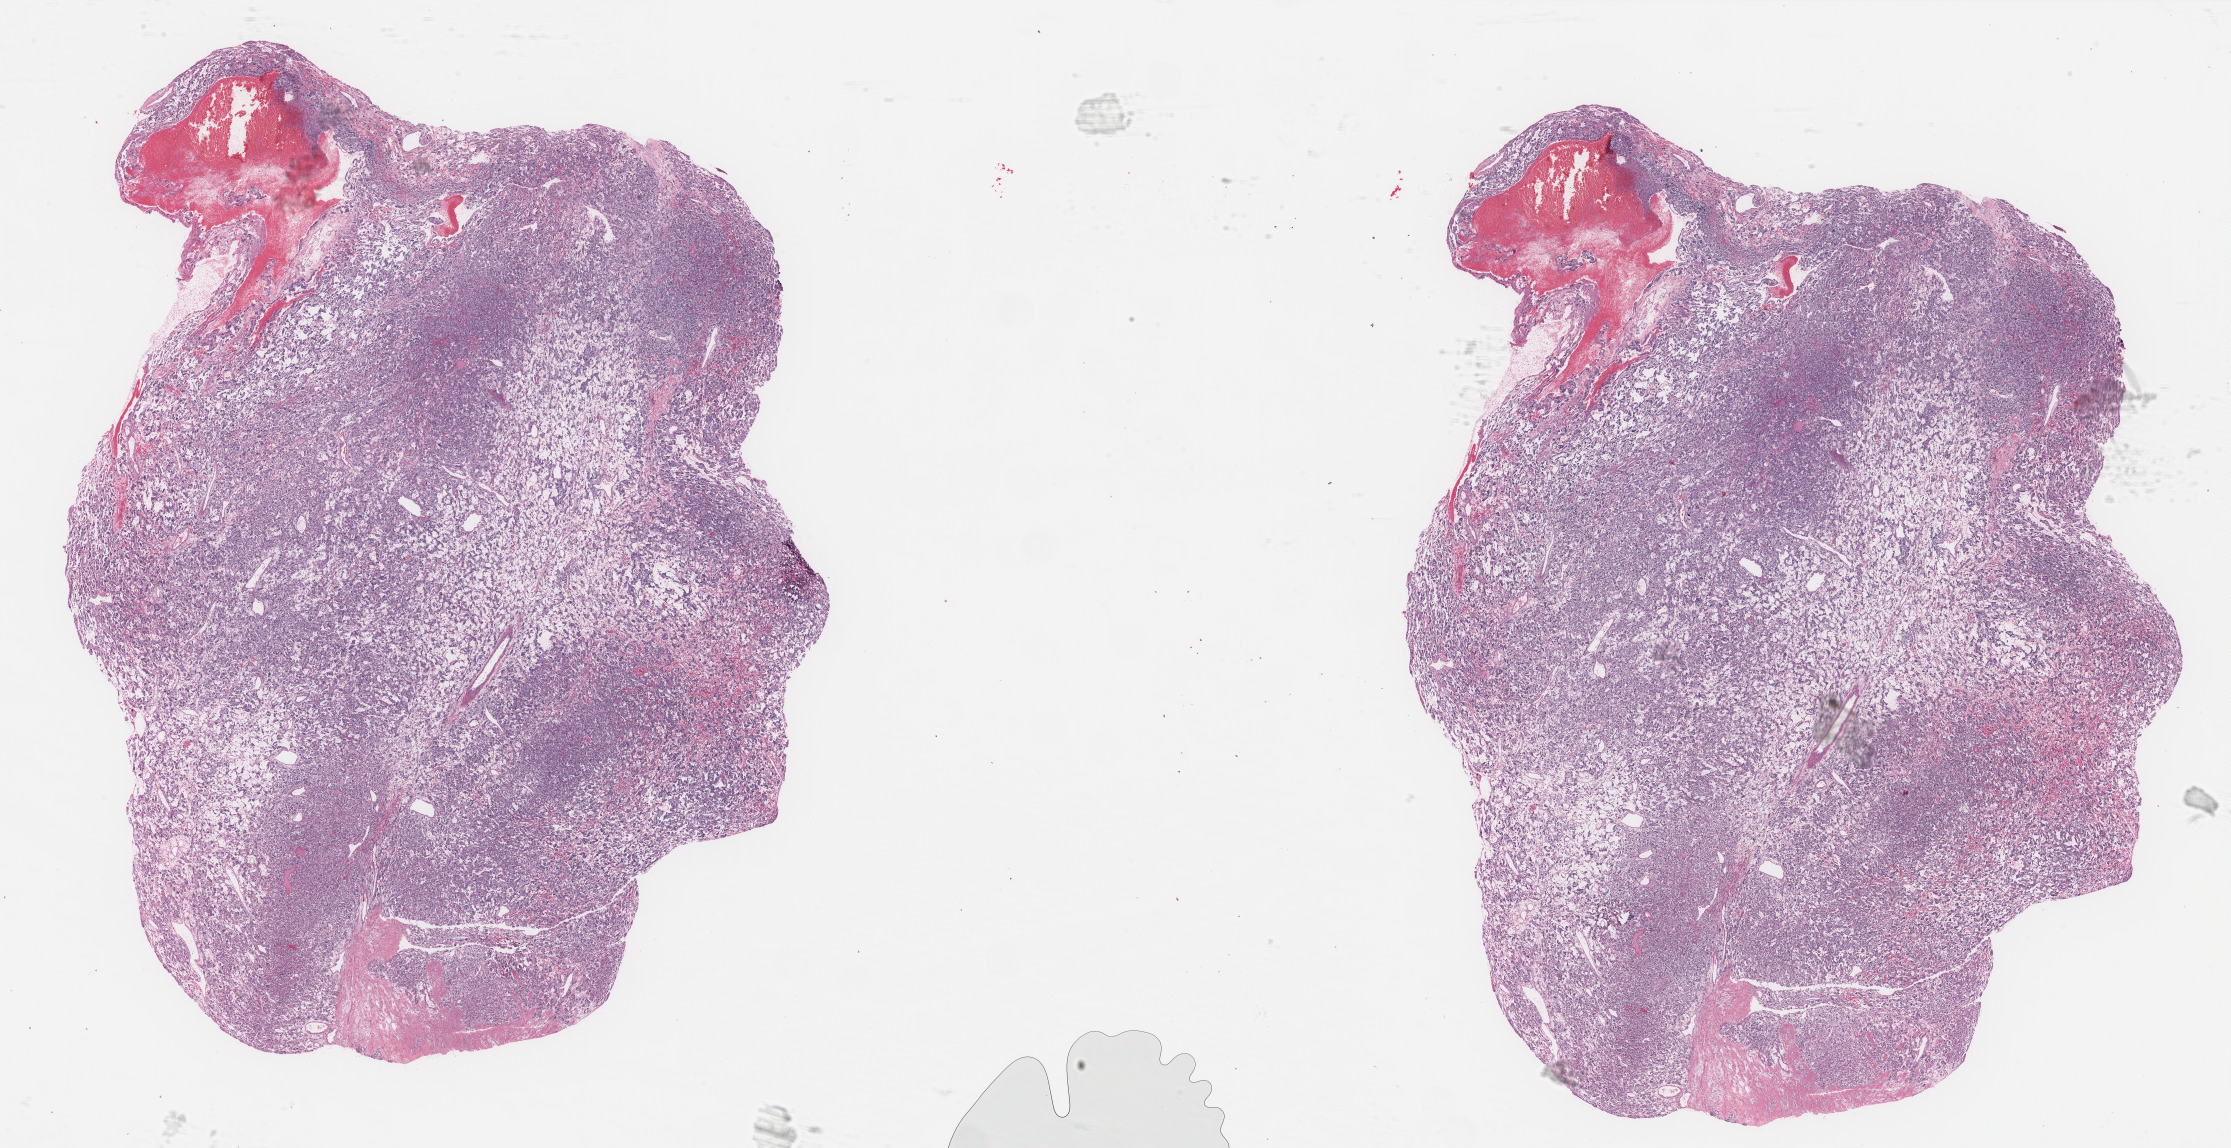
H&E-stained whole-slide image — a low-resolution overview of the entire scanned area, about 35.3 x 18.2 mm (from a 40x scan); formalin-fixed paraffin-embedded (FFPE) diagnostic section; primary tumour sample from the adrenal gland. Patient: male, age at initial diagnosis 27 years.
* diagnosis: Pheochromocytoma, malignant
* laterality: left